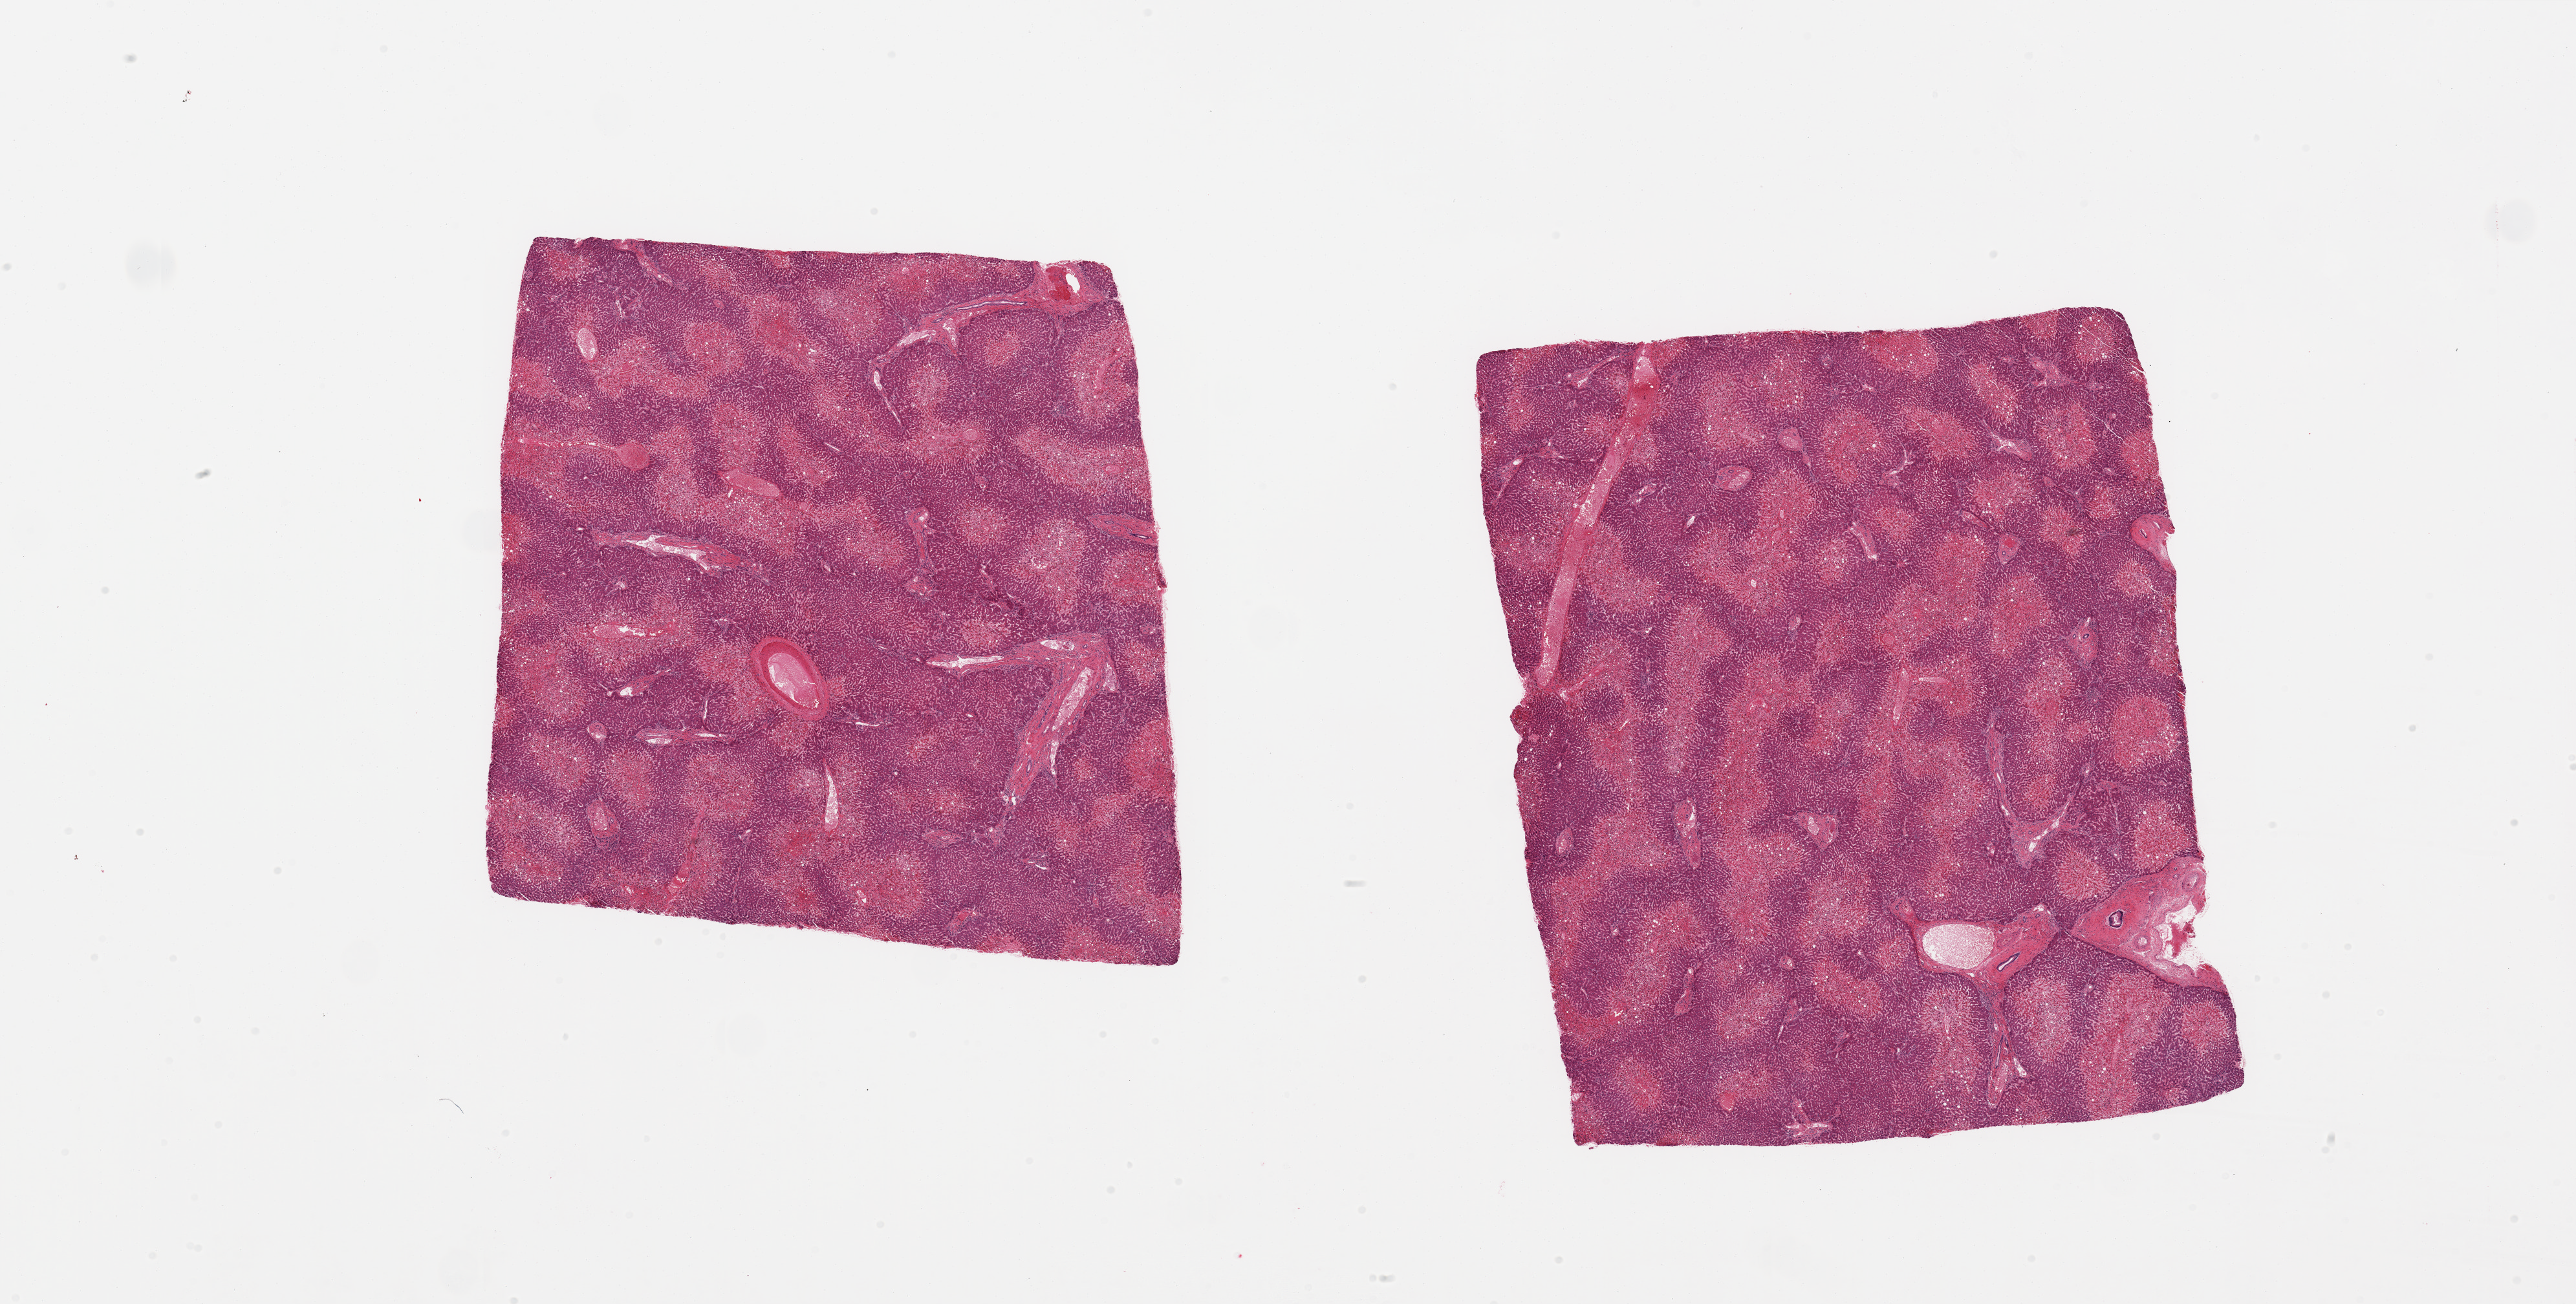
H&E whole-slide image — a low-resolution overview of the entire scanned area, about 31.5 x 16.0 mm; PAXgene-fixed paraffin-embedded (PFPE) section; sampled site (target tissue): liver; tissue donor sample. Donor sex: male.
• pathologist's review note for this sample: 2 pieces, moderate-severe subacute chronic congestion